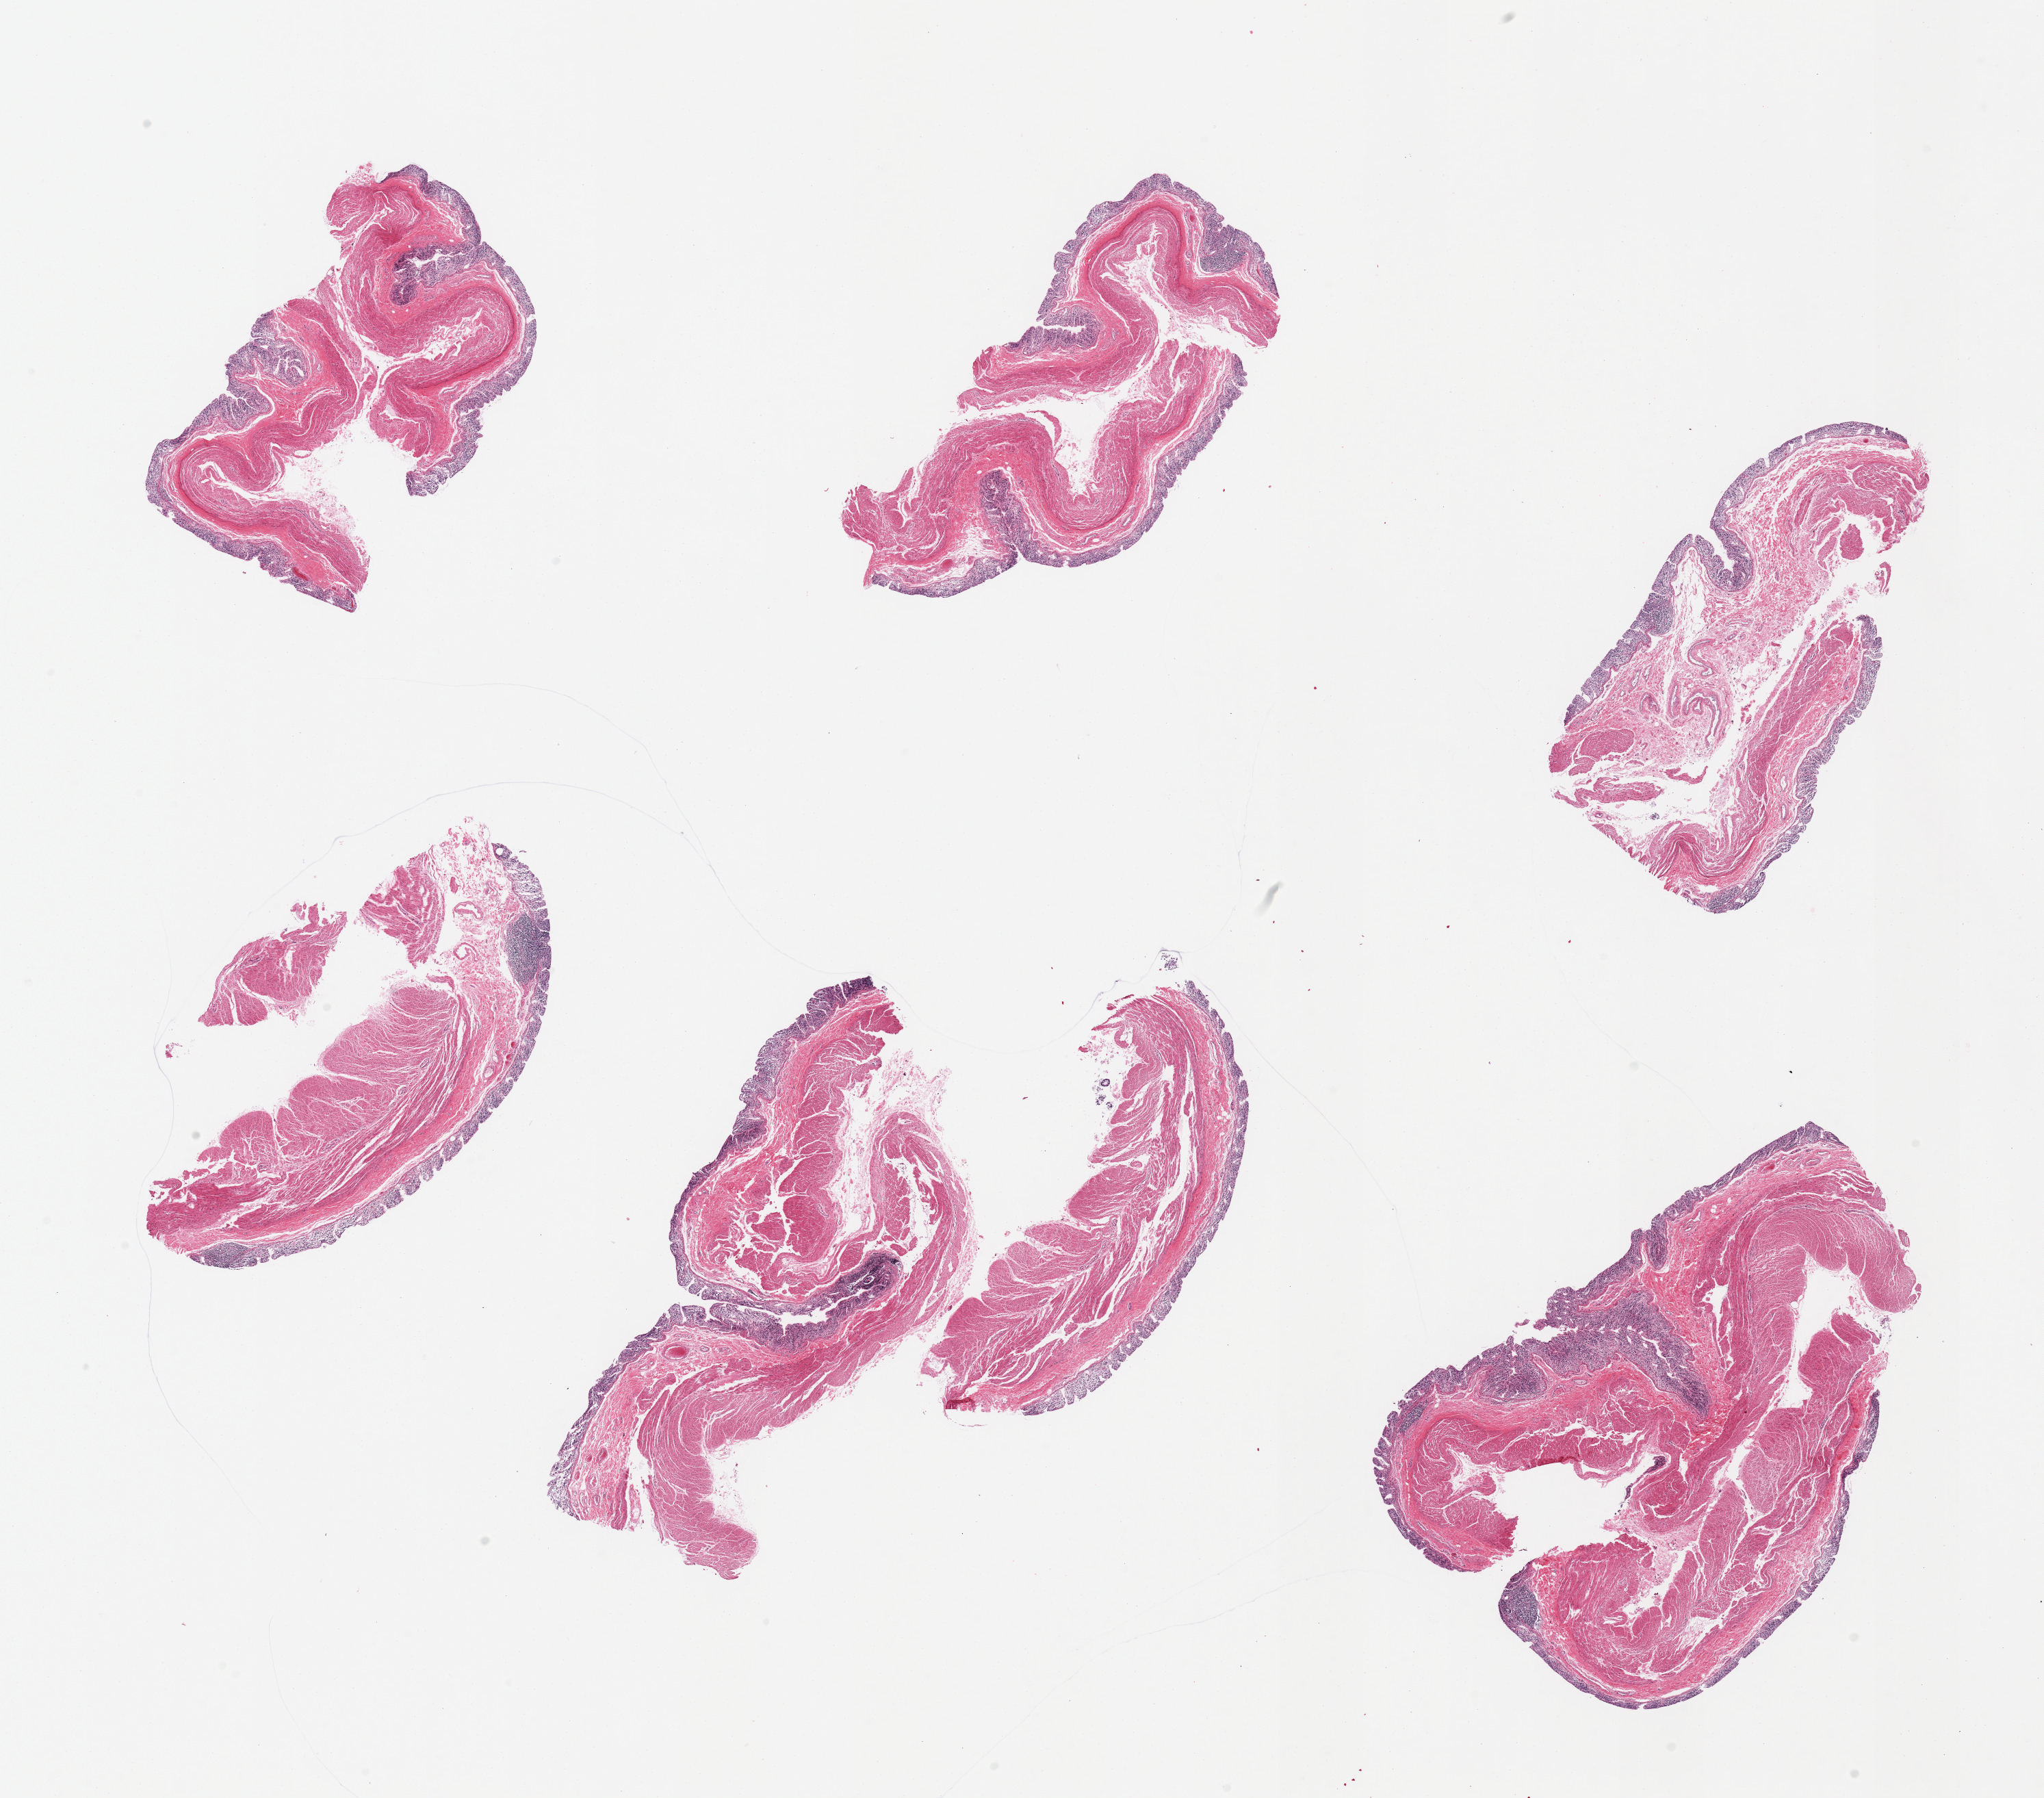
Digitized haematoxylin and eosin-stained section, low-resolution overview of the scanned area, about 23.6 x 20.8 mm (slide scanned at 20x). PAXgene-fixed, paraffin-embedded tissue. Sampled site (target tissue): transverse colon. Tissue donor sample. Donor sex: male.
Pathologist's review note for this sample: 6 pieces; moderate to severe mucosal autolysis and preserved muscularis.